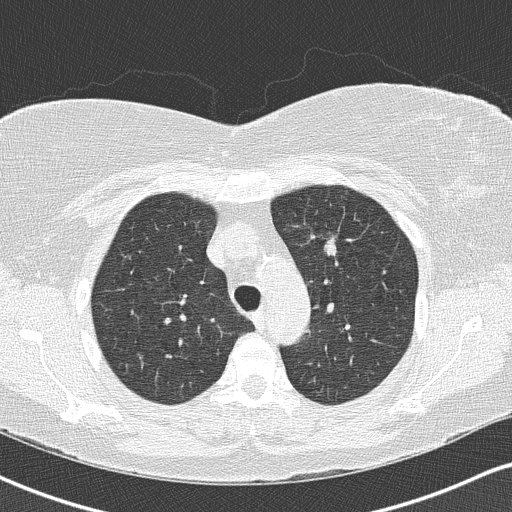
Low-dose screening chest CT, axial slice, second screening round (one year after baseline), lung window (W 1500 / L -600 HU), 2 mm slice thickness, lung (sharp) reconstruction kernel (B50f), 512 × 512 image matrix, field of view 328 × 328 mm. Female participant, aged 57 years at enrolment. Current smoker at enrolment.
Expert-annotated lung lesion, bounding box <313,225,348,266> (left, top, right, bottom; pixels). The screening reader recorded 3 non-calcified nodules or masses ≥4 mm on this exam (left upper lobe, right upper lobe, right middle lobe); which of them this box marks is not recorded. Participant outcome: lung cancer diagnosed 75 days after this screen — adenocarcinoma, NOS, left upper lobe, poorly differentiated (G3), stage IA (AJCC 6th edition), 24 mm at pathology.